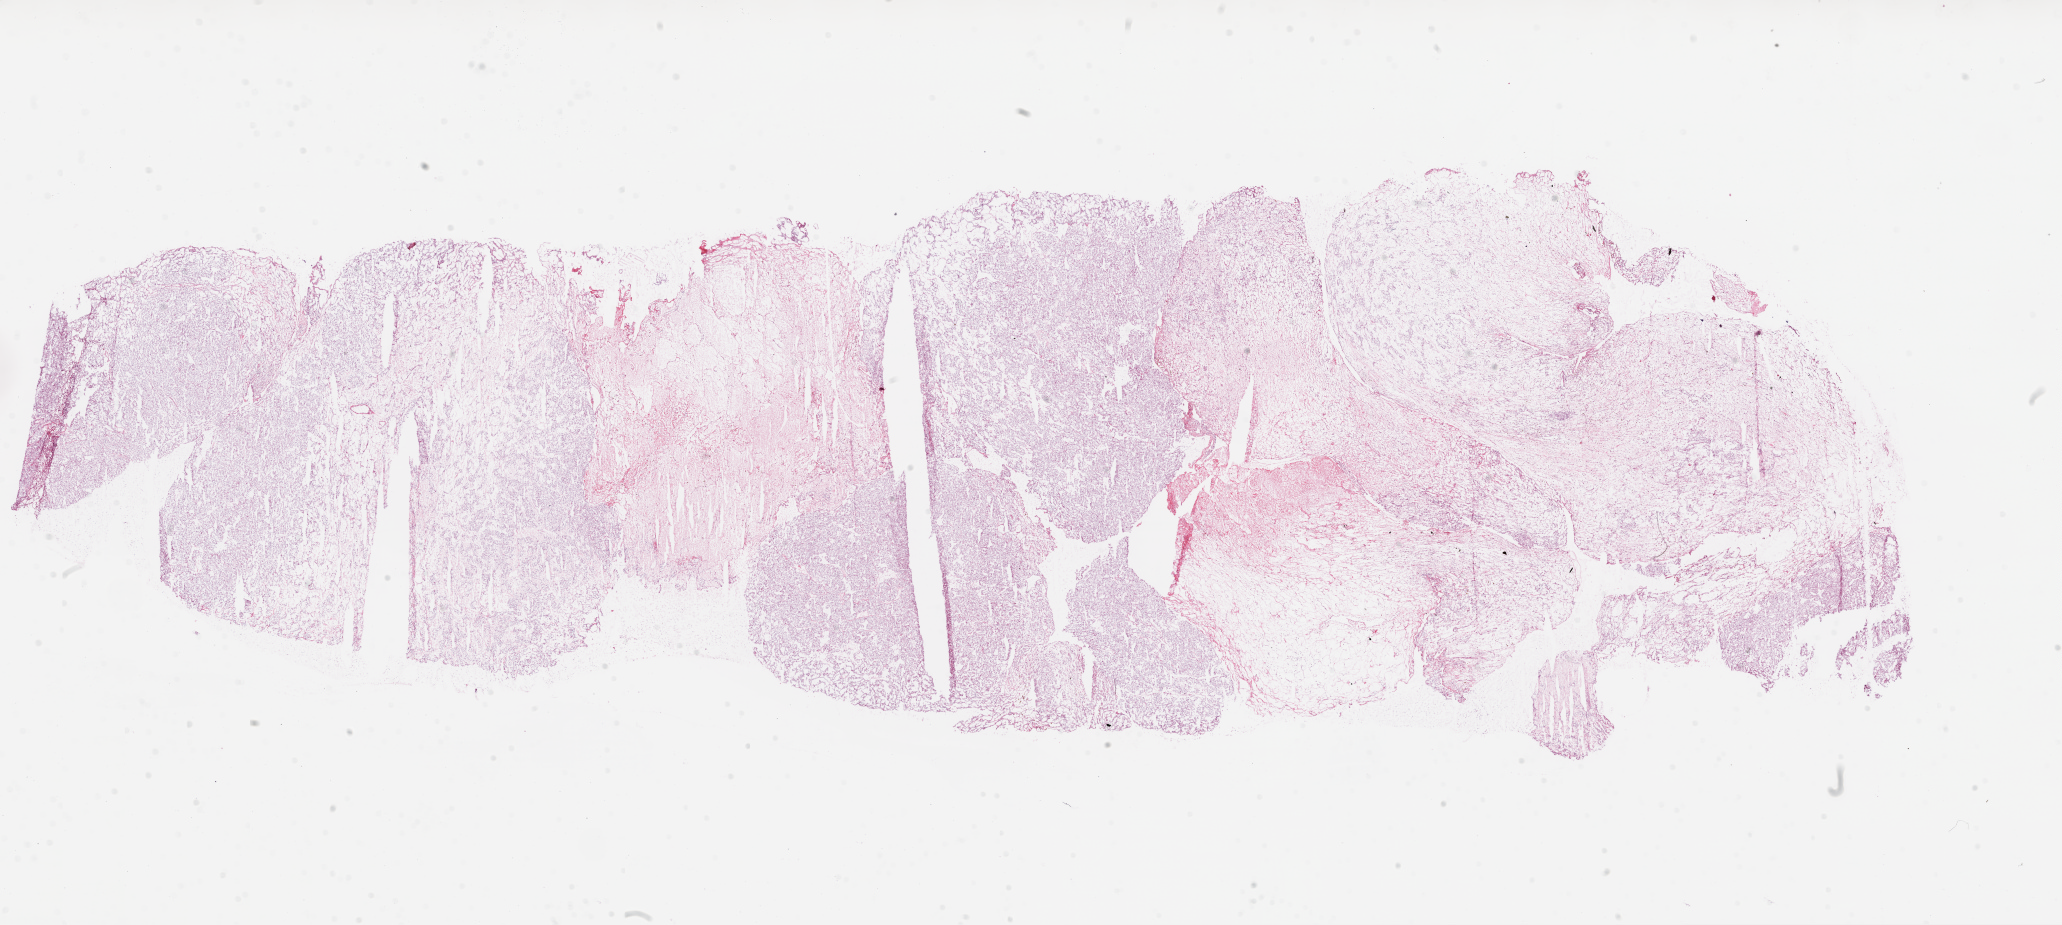
H&E whole-slide image, low-resolution overview of the scanned area, about 33.1 x 14.8 mm (acquisition: 20x scan). Frozen section. Primary tumour sample from the kidney. Female, age 60 years at initial diagnosis. Histologic grade: G2 (moderately differentiated). Composition of this section per pathologist review: tumour cells 70%, tumour nuclei 80%, normal cells 0%, stromal cells 30%, necrosis 0%.
Laterality: right. Histologic diagnosis: Clear cell adenocarcinoma, NOS. AJCC pathologic stage: I (7th edition).